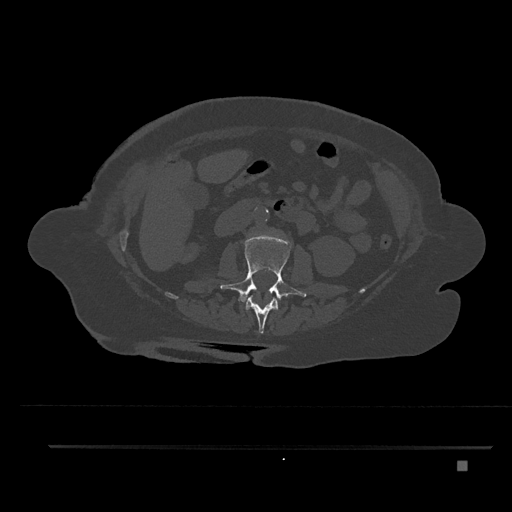
CT including the spine, one axial slice. Slice 180 of 797 in the series (ordered by position). Bone window (W 1800 / L 400 HU). 0.5 mm slice thickness. 512 × 512 image matrix, field of view 437 × 437 mm. Patient: female, 76 years. Case-level facts recorded for this patient, not image findings: primary cancer: lung.
Outlined on this slice (semi-automatically segmented with operator editing):
- L1 vertebra: bounding box <245,295,279,334> (left, top, right, bottom; pixels)
- L2 vertebra: <220,235,307,303>